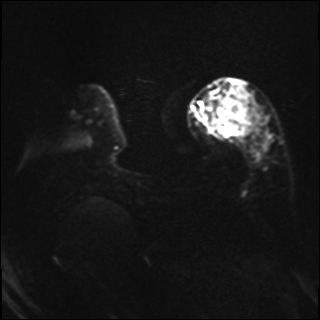
Breast MRI, one axial slice. Slice 7 of 37 in the series (ordered by position). Diffusion-weighted series; image 2 of 4 stored at this slice position (different b-values; order by instance number). 1.5 T. 4 mm slice thickness. 320 × 320 image matrix. Female patient.
Structures marked on this image (outlined manually by an expert reader):
- tumour on diffusion-weighted imaging: bounding box <221,94,257,129> (left, top, right, bottom; pixels)